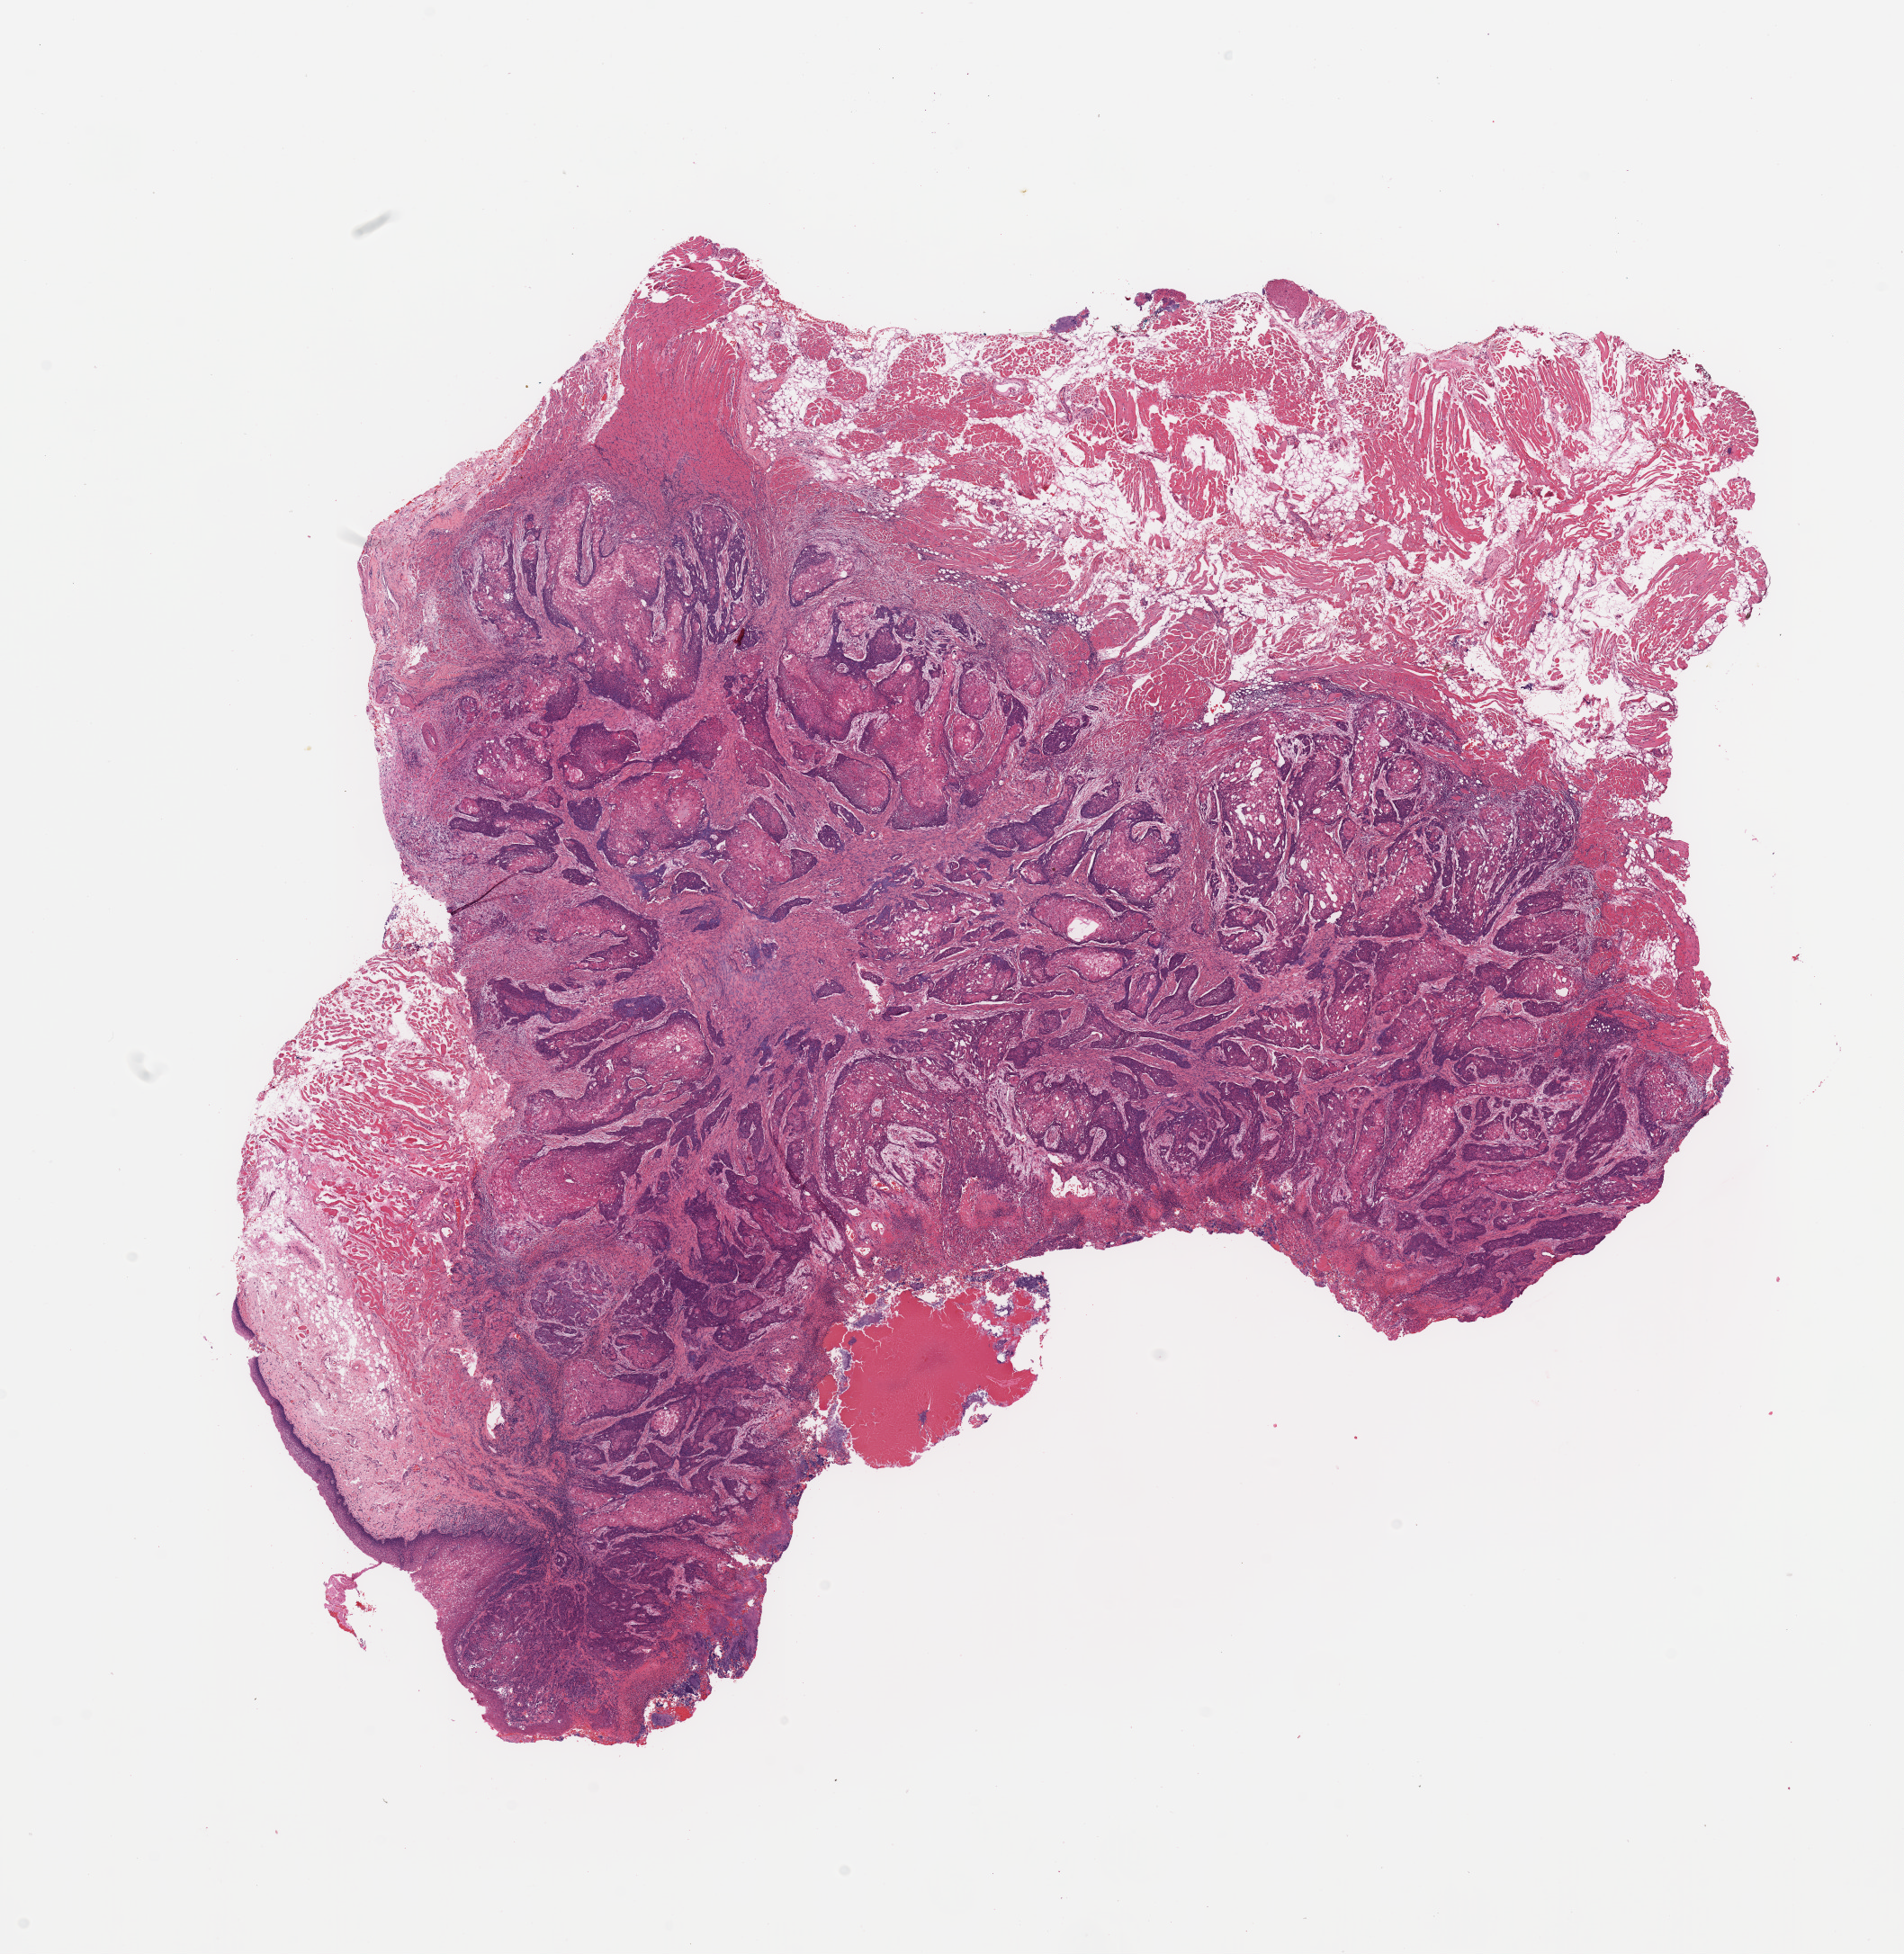
Whole-slide histology image, Hematoxylin and eosin (H&E) stained, whole scanned area (about 16.7 x 17.2 mm) shown as a low-resolution overview. Head and neck, tissue type not recorded. 61-year-old male patient.
* patient diagnosis: Squamous cell carcinoma, NOS (tongue, NOS)